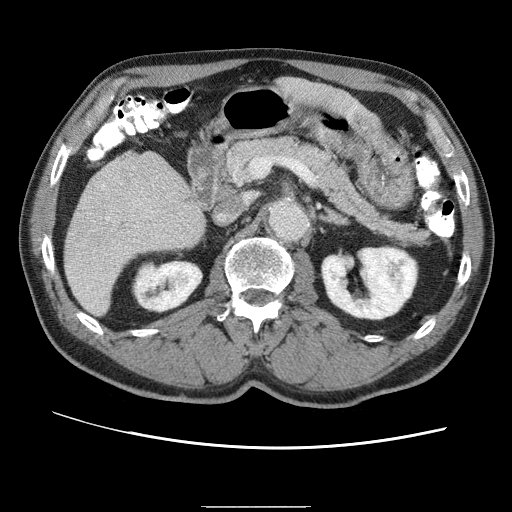
Contrast-enhanced abdominal CT (liver protocol), one axial slice. Slice 18 of 75 in the series (ordered by position). Reconstruction kernel STANDARD. One of 2 acquisitions stored at this slice position. Soft-tissue window (W 400 / L 40 HU). 2.5 mm slice thickness. 512 × 512 image matrix, field of view 360 × 360 mm. From the clinical record (not read from this slice): diagnosis: hepatocellular carcinoma (patient treated with transarterial chemoembolisation; whether this scan precedes or follows treatment is not stated here); TNM stage (as recorded): Stage-II.
Structures marked on this image (semi-automatically segmented with operator editing):
- liver parenchyma outside the tumour (the mass and vessels are separate outlines, so this box may not span the whole liver): bounding box <64,156,198,312> (left, top, right, bottom; pixels)
- liver vessels: <98,177,149,274>